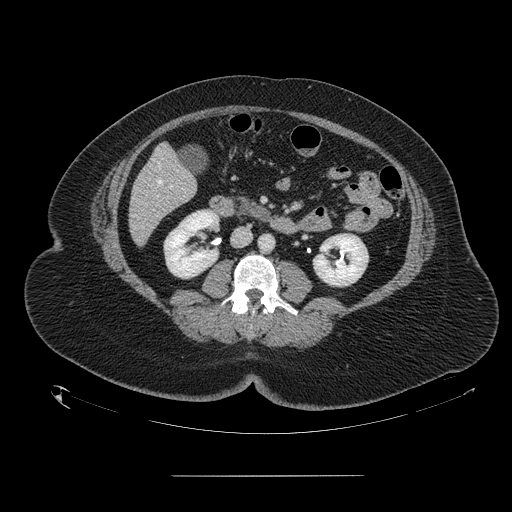
Contrast-enhanced abdominal CT, one axial slice. Intravenous contrast given. Soft-tissue window (W 400 / L 40 HU). 2.5 mm slice thickness. 512 × 512 image matrix, field of view 495 × 495 mm. Female patient, age 52 years. Case-level facts recorded for this patient, not image findings: diagnosis: colorectal cancer liver metastases, imaged before liver resection.
Annotated regions visible in this slice (expert manual segmentation):
- hepatic veins: bounding box (x1, y1, x2, y2) in pixels: (158, 164, 161, 184)
- liver: (130, 145, 196, 245)